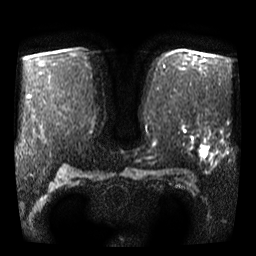
Breast MRI, one axial slice; slice 28 of 46 in the series (ordered by position); diffusion-weighted series; image 2 of 4 stored at this slice position (different b-values; order by instance number); 3 T; 5 mm slice thickness; 256 × 256 image matrix, field of view 340 × 340 mm. Female patient.
Annotated regions visible in this slice (manually delineated by an expert):
- tumour on diffusion-weighted imaging: bounding box [x1, y1, x2, y2] px = [200, 146, 209, 157]